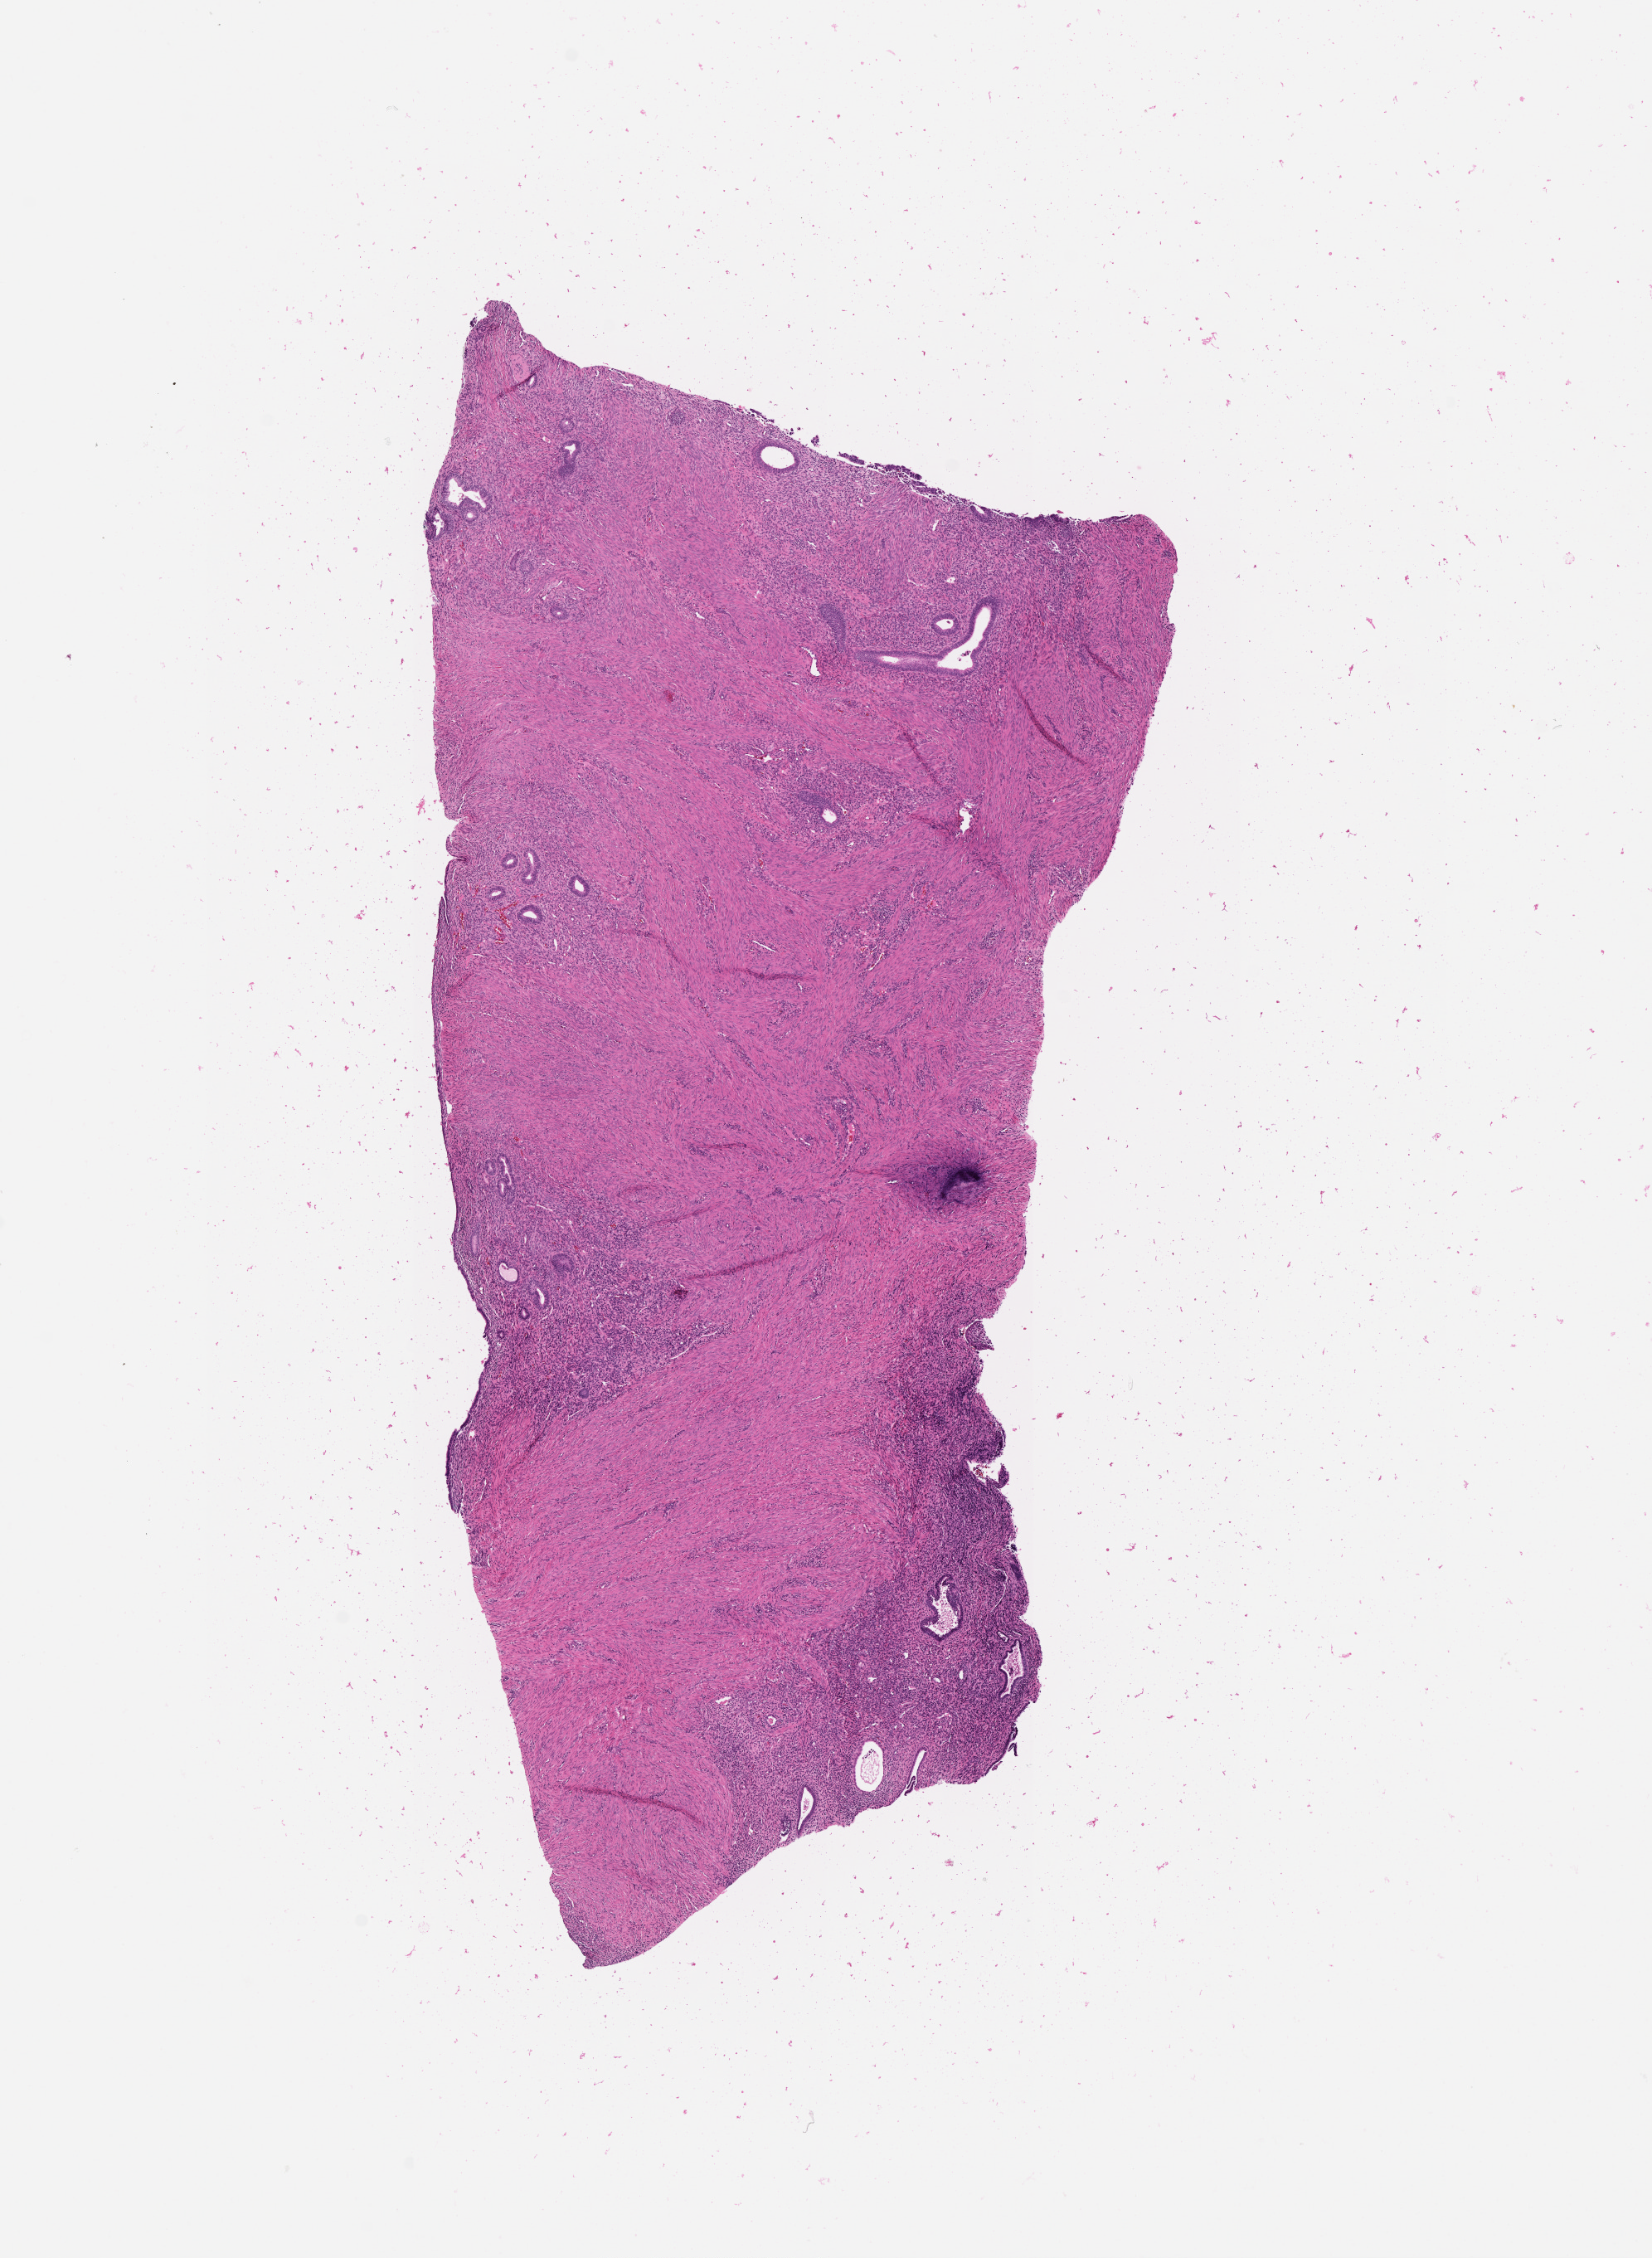
Whole-slide histology image, H&E-stained — low-resolution overview of the scanned area, about 8.0 x 11.0 mm. Uterus, normal (non-tumour) tissue. Patient: female, age 68 years.
* this section: normal (non-tumour) tissue from the same patient
* patient diagnosis: Endometrioid adenocarcinoma, NOS